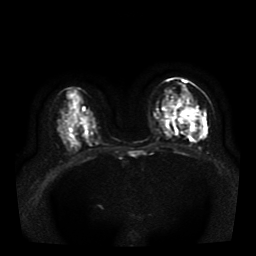
Breast MRI, one axial slice; slice 19 of 41 in the series (ordered by position); diffusion-weighted series; image 2 of 4 stored at this slice position (different b-values; order by instance number); 1.5 T; 256 × 256 image matrix, field of view 330 × 330 mm. Female patient.
Structures marked on this image (outlined manually by an expert reader):
- tumour on diffusion-weighted imaging: bounding box (x1, y1, x2, y2) in pixels: (178, 108, 204, 137)